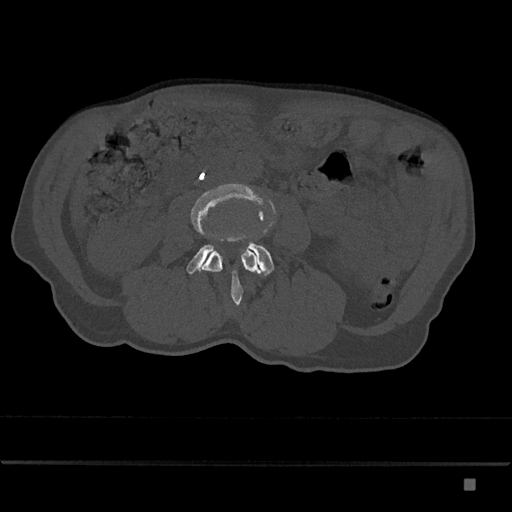
CT including the spine, one axial slice; slice 375 of 797 in the series (ordered by position); reconstruction kernel Br40s/3; 120 kVp; bone window (W 1800 / L 400 HU); 0.5 mm slice thickness; 512 × 512 image matrix, field of view 390 × 390 mm. Male patient, age 72 years. From the clinical record (not read from this slice): primary cancer: prostate.
Outlined on this slice (semi-automatic segmentation, software-assisted and operator-edited):
- L3 vertebra: bounding box <190,183,267,306> (left, top, right, bottom; pixels)
- L4 vertebra: <186,241,274,277>